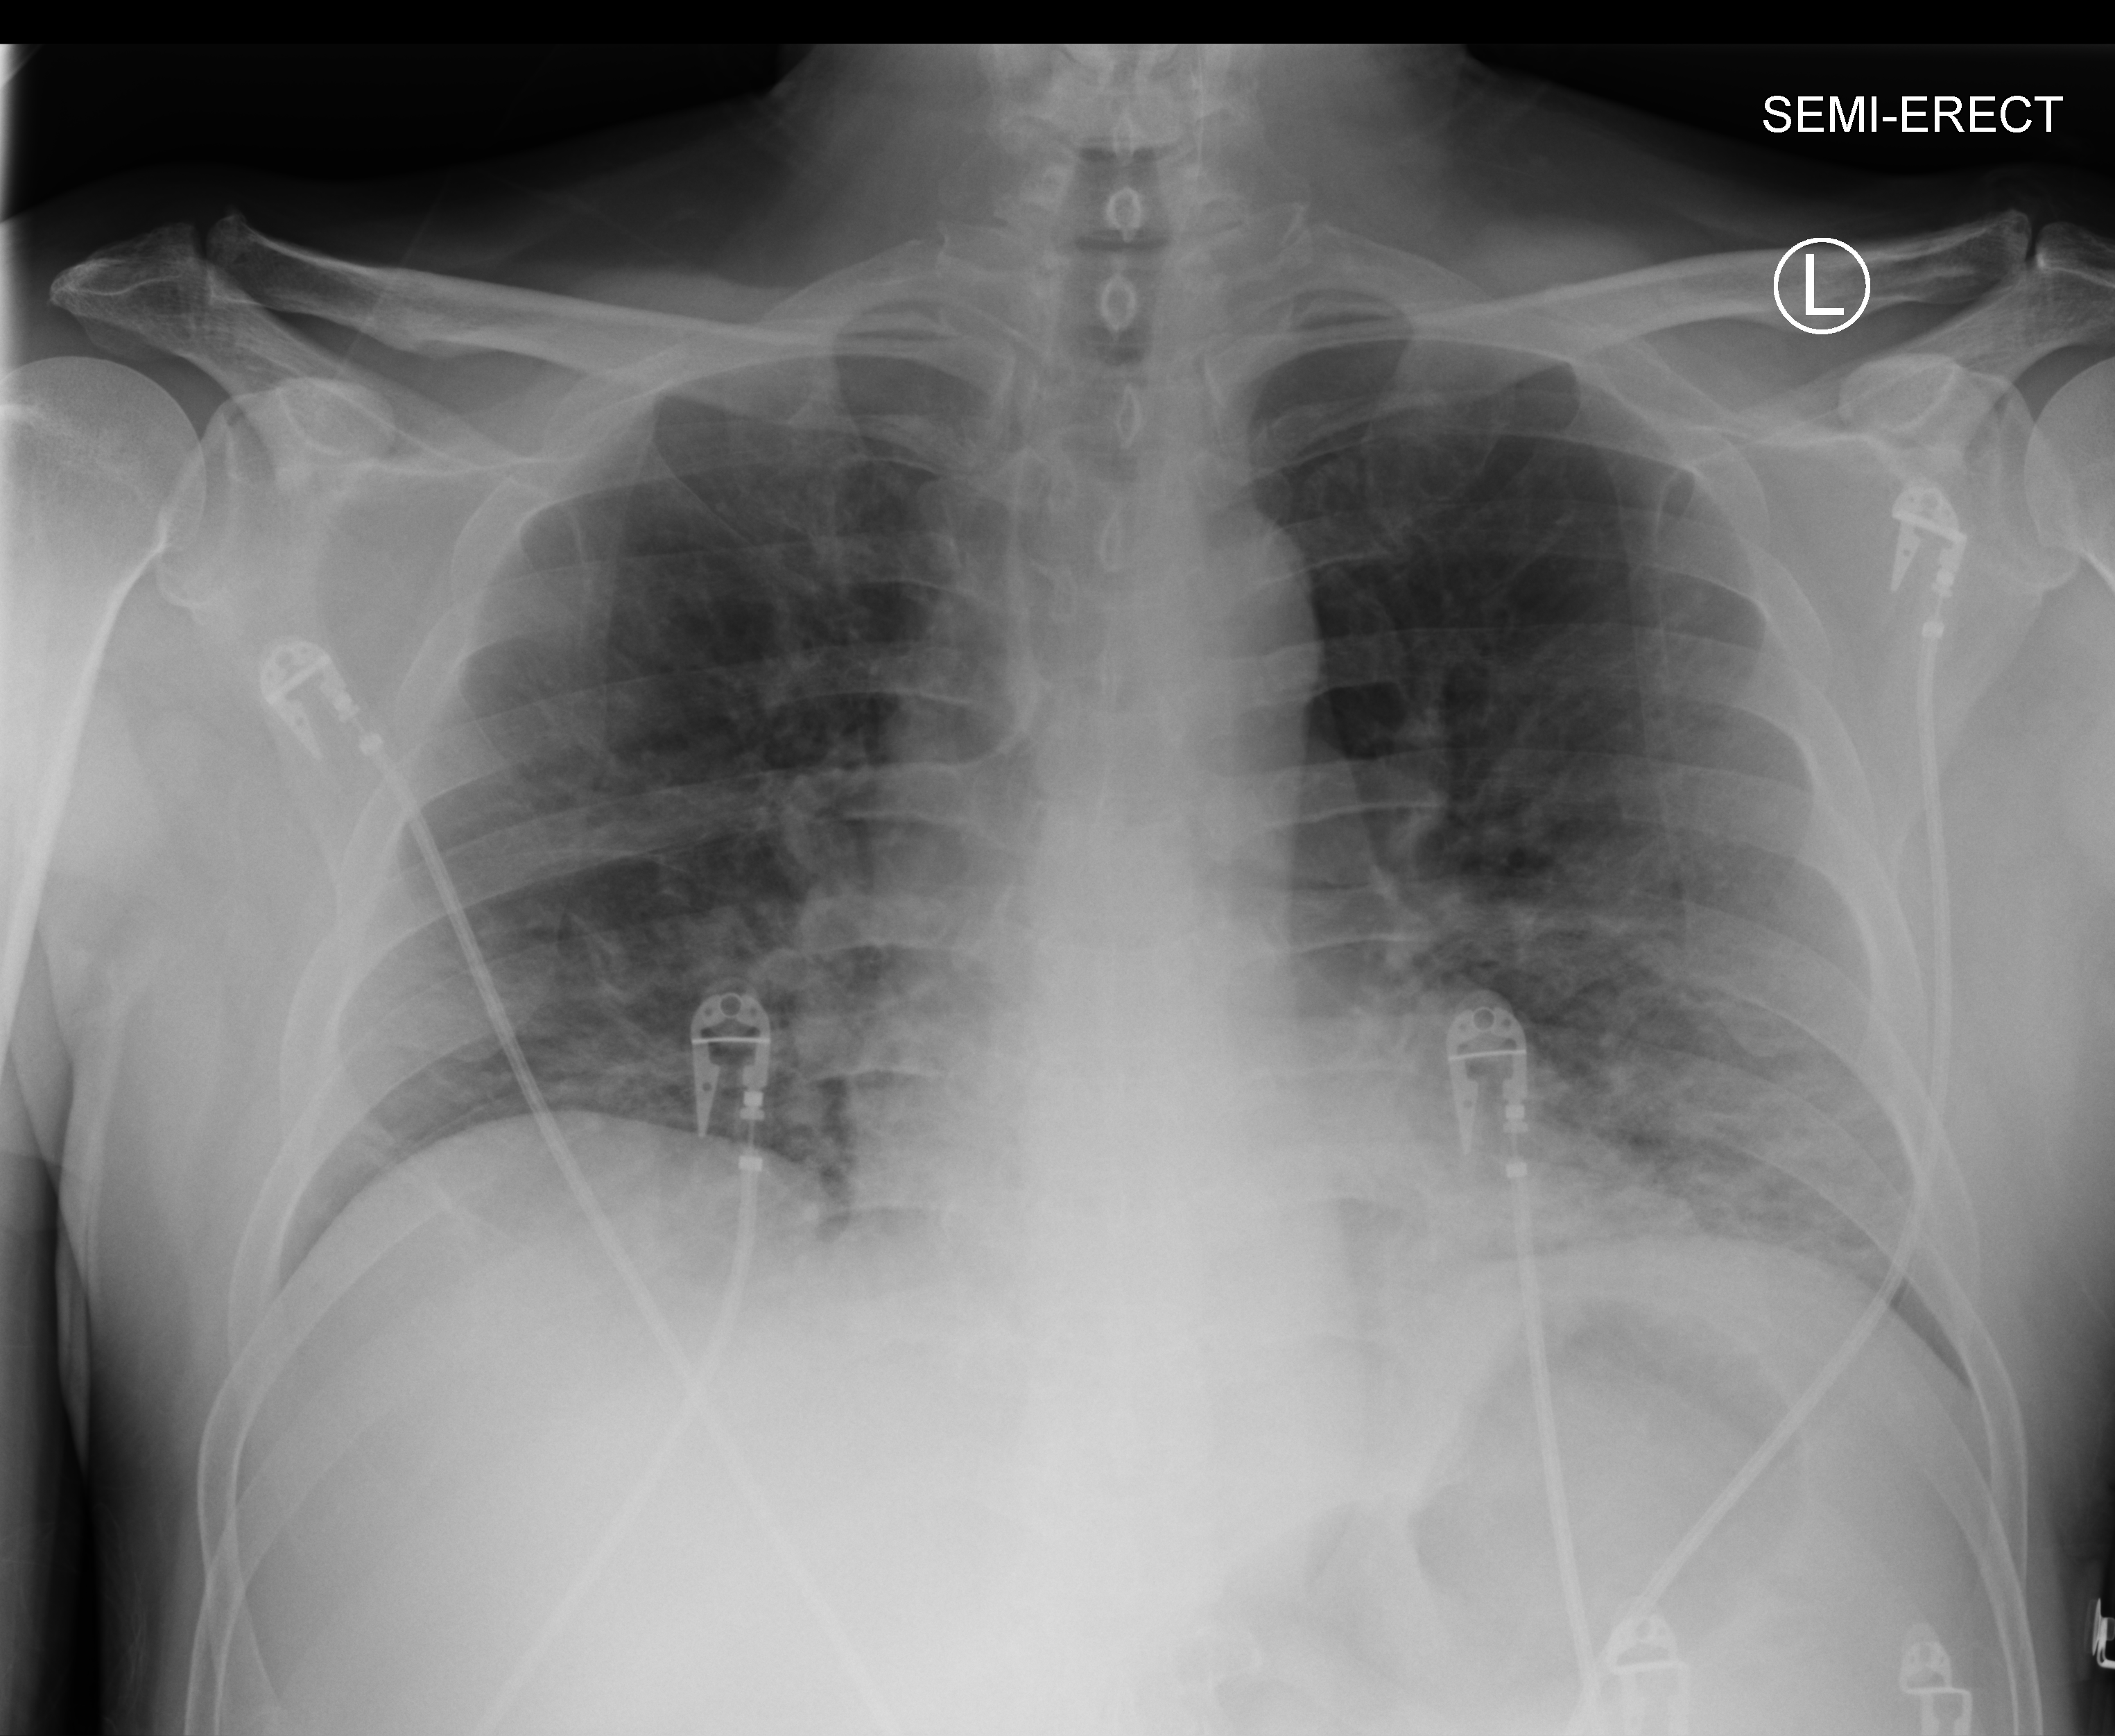
Portable chest radiograph; anteroposterior (AP) projection. Male patient hospitalised with COVID-19, age 18–59 years.
From the hospital-stay record, not from the radiograph (when in the stay this image was taken is not recorded):
- diabetes (admission record): yes